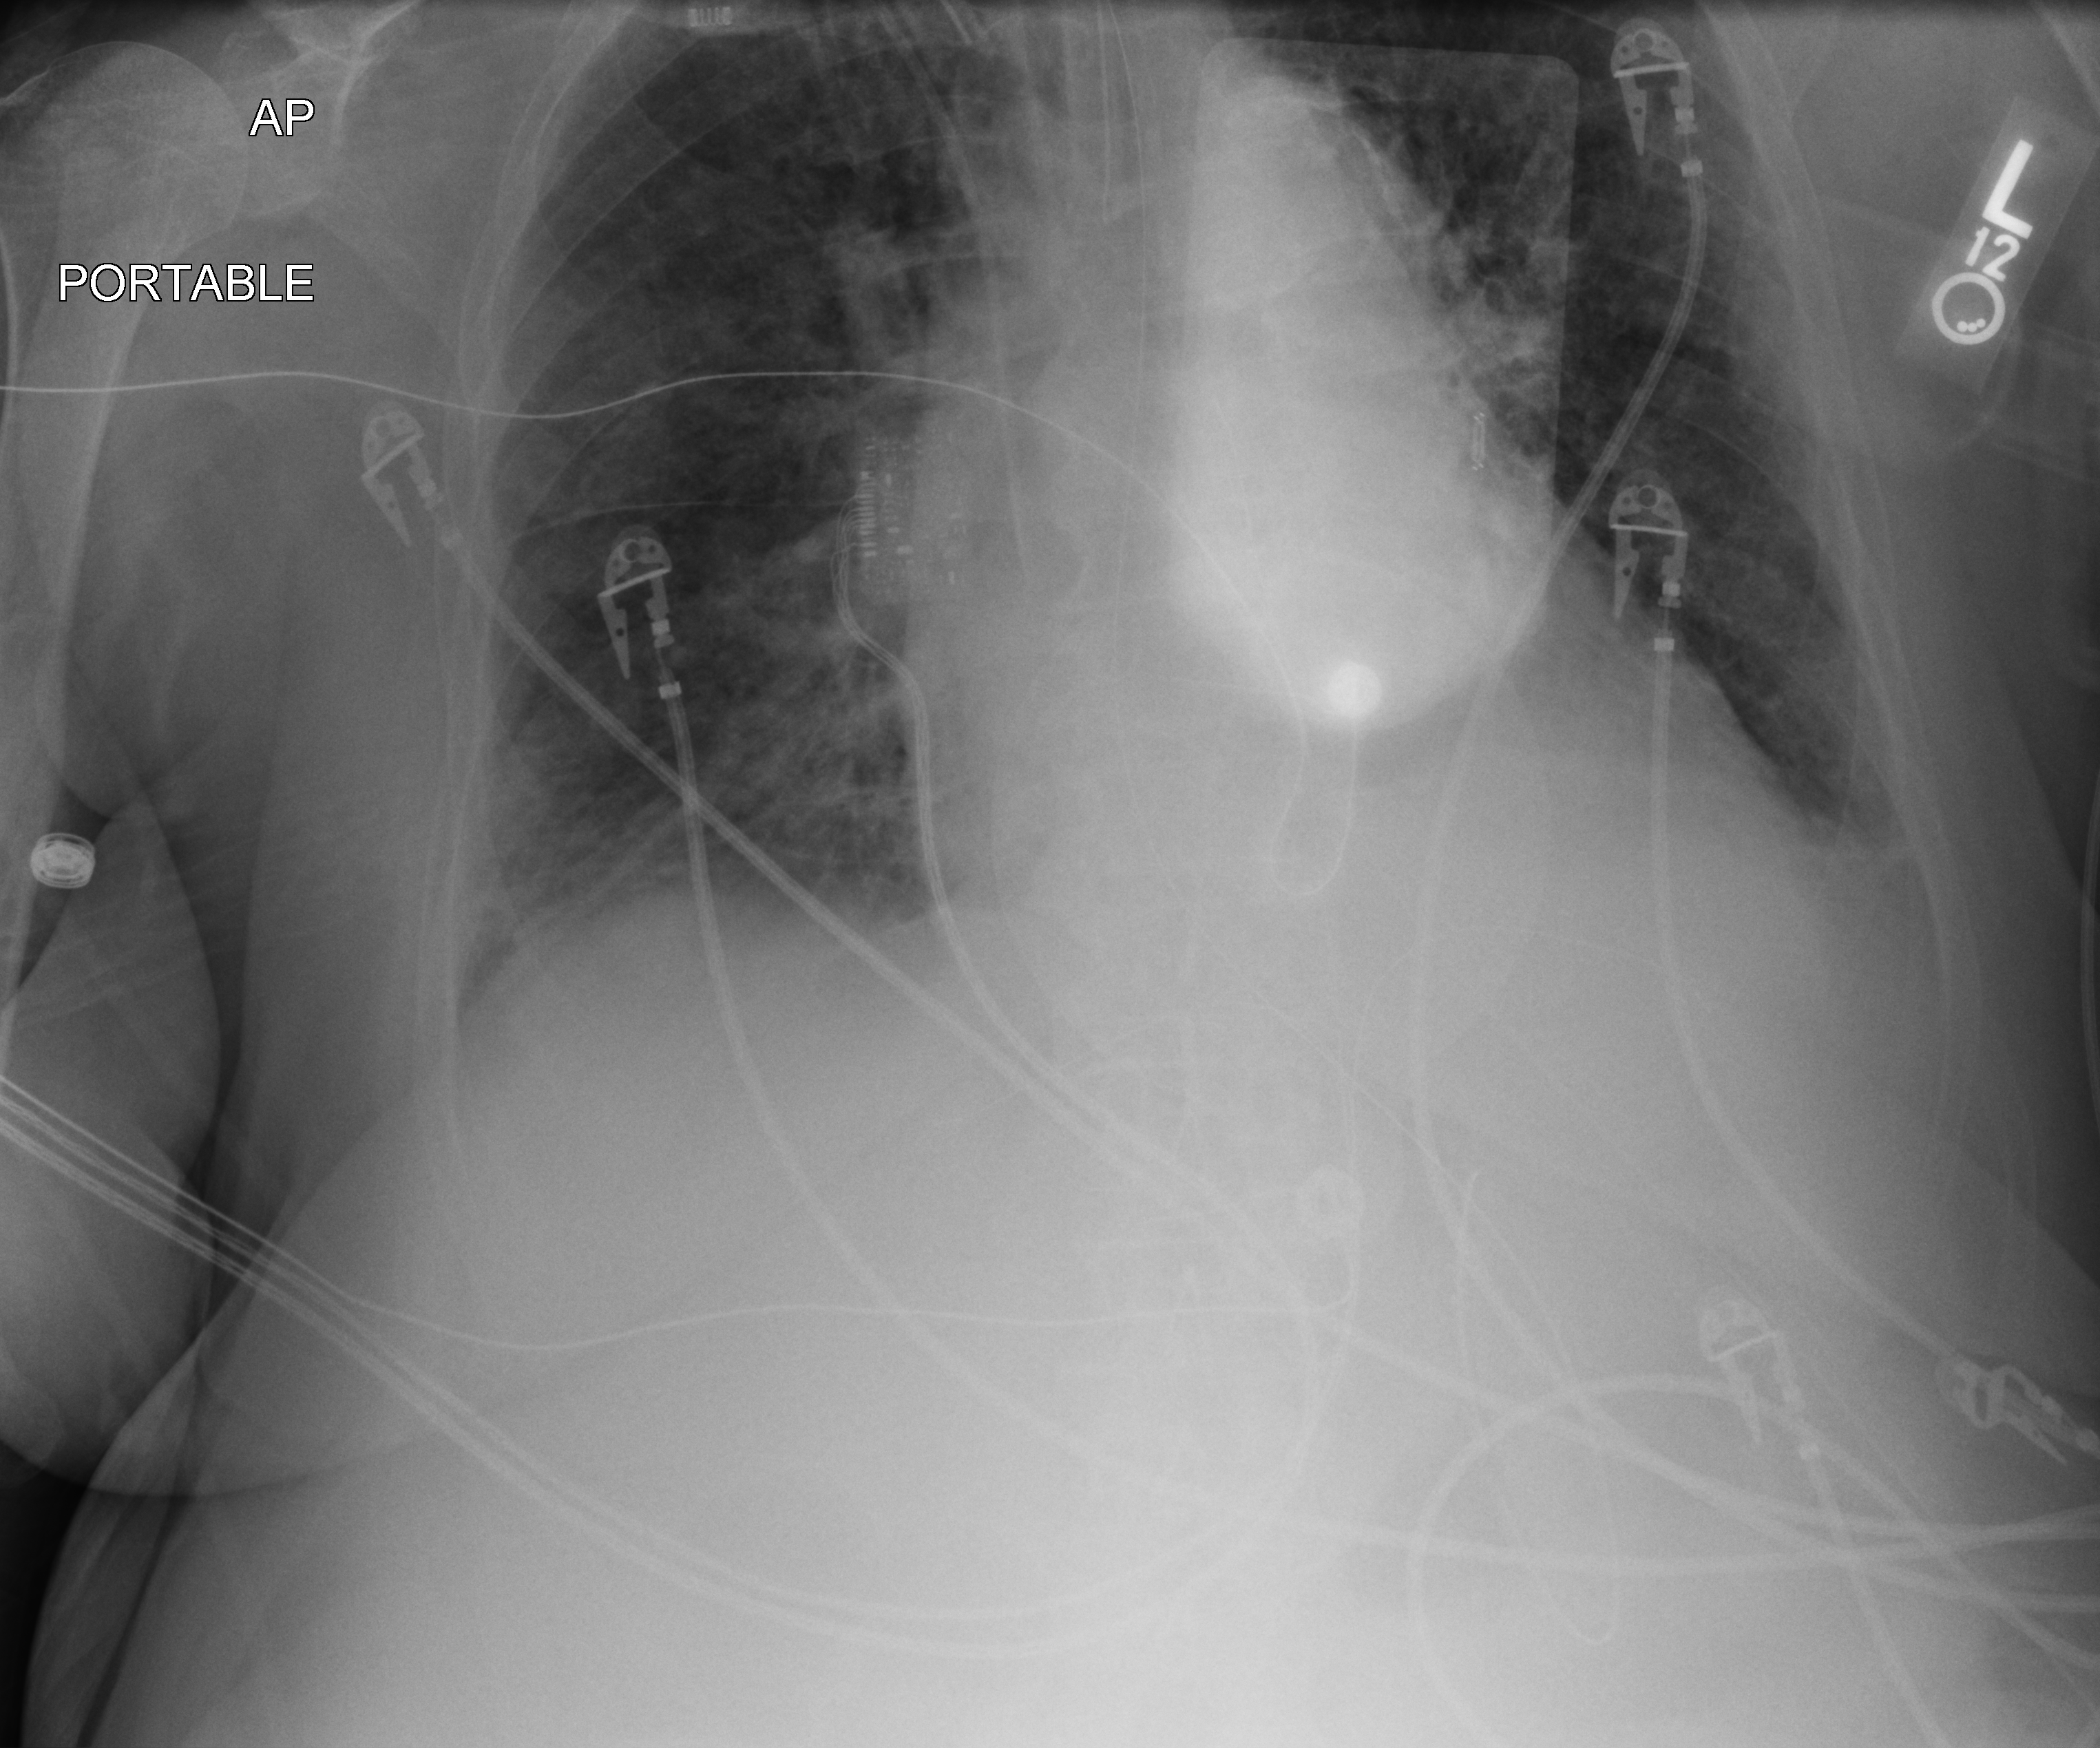
Chest X-ray (portable); anteroposterior (AP) projection. Patient hospitalised with COVID-19; female, aged 75–90 years.
Hospital-stay facts (about this admission, not read from this image; timing relative to this image not recorded):
- mechanically ventilated during this hospital stay: yes
- admitted to intensive care during this hospital stay: yes